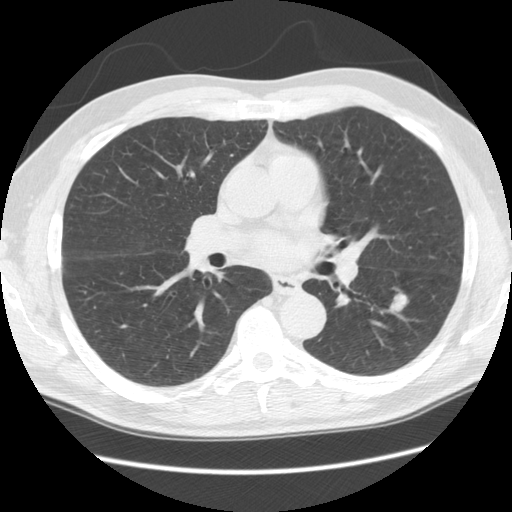
Low-dose screening chest CT, one axial slice; position 57 of 111 along the scan axis; 120 kVp; lung window (W 1500 / L -600 HU); 2.5 mm slice thickness; 512 × 512 image matrix.
Outlined on this slice (expert manual segmentation):
- lesion 1 (tumor, lower lobe of left lung): bounding box <390,294,407,312> (left, top, right, bottom; pixels)